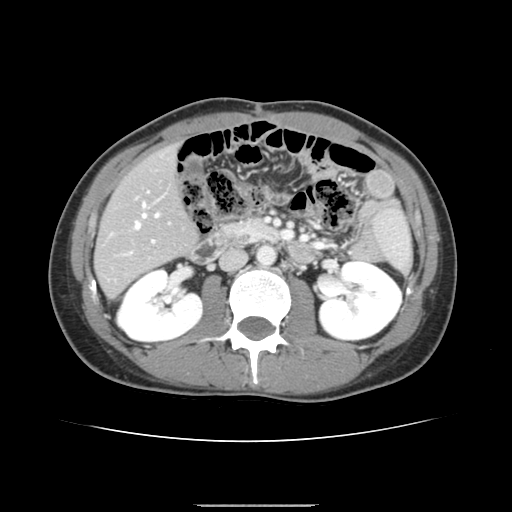
Contrast-enhanced abdominal CT, one axial slice. Position 63 of 150 along the scan axis. 120 kVp. Intravenous contrast given. Soft-tissue window (W 400 / L 40 HU). 512 × 512 image matrix, field of view 324 × 324 mm. Female patient, age 32 years. From the clinical record (not read from this slice): diagnosis: colorectal cancer liver metastases, imaged before liver resection; multiple liver metastases: yes; largest metastasis: 0.7 cm; disease in both lobes: no.
Outlined on this slice (outlined manually by an expert reader):
- hepatic veins: bounding box [x1, y1, x2, y2] px = [135, 203, 159, 229]
- liver: [96, 148, 196, 298]
- planned liver remnant (the part of the liver to remain after resection): [96, 148, 196, 294]
- portal vein (with intrahepatic branches): [129, 191, 154, 253]